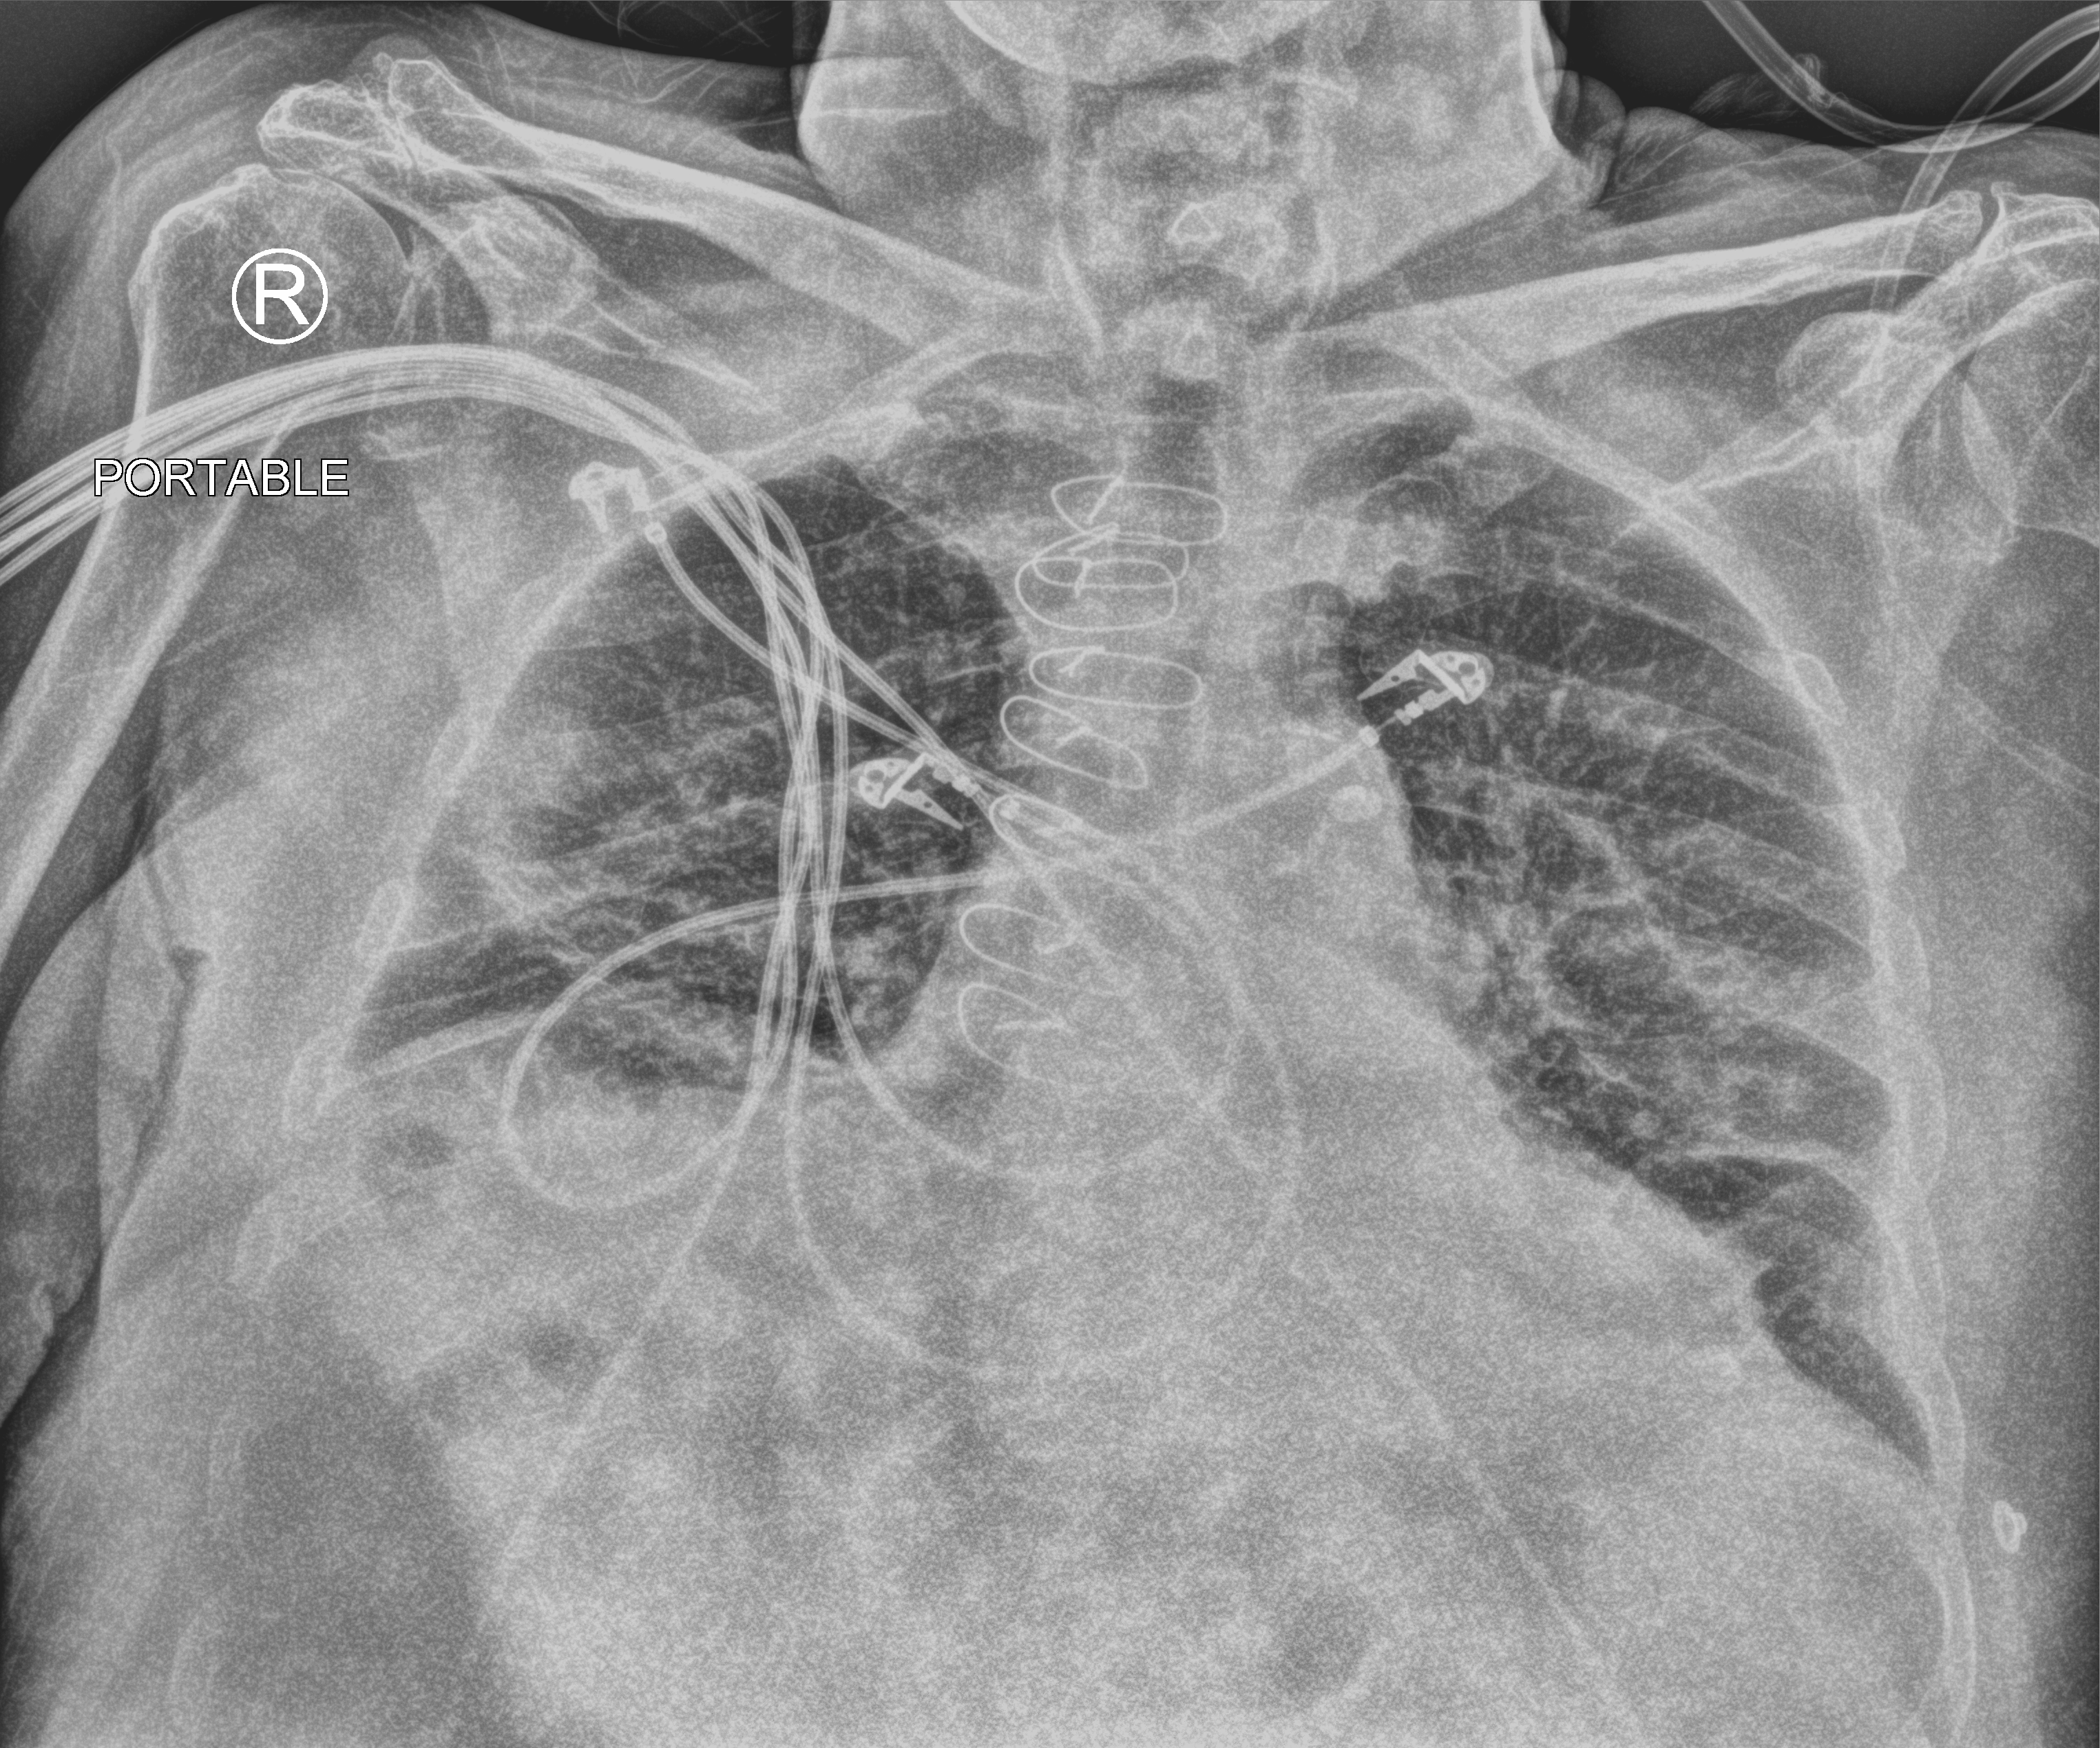
Chest X-ray (portable), anteroposterior (AP) projection. Patient hospitalised with COVID-19; male, aged 75–90 years.
Hospital-stay facts (about this admission, not read from this image; timing relative to this image not recorded):
- admitted to intensive care during this hospital stay: no